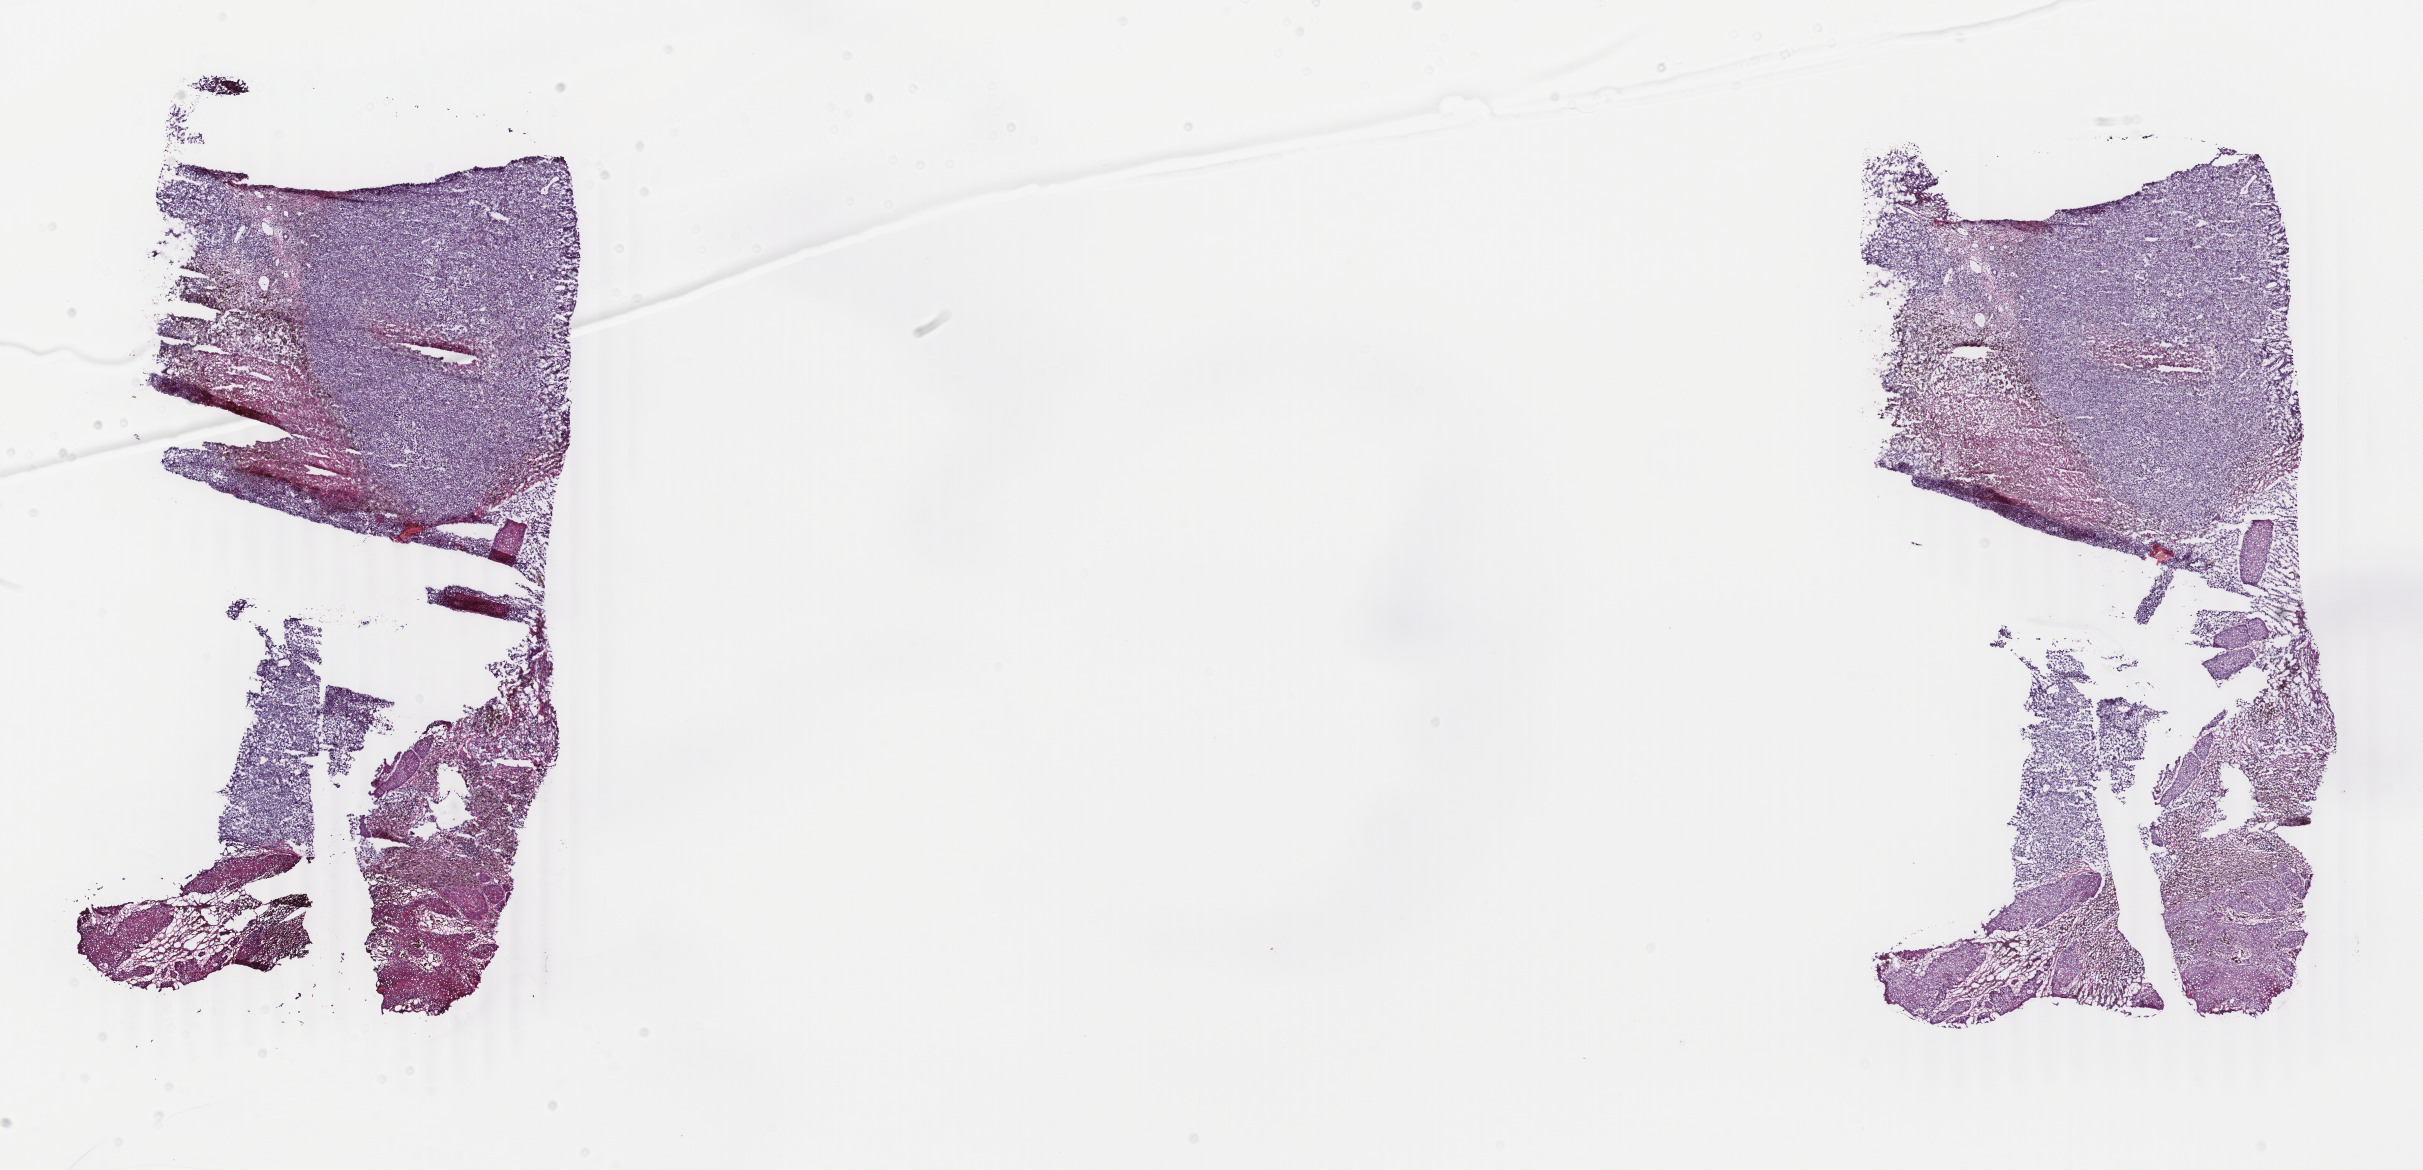
Hematoxylin and eosin (H&E) stained whole-slide image — whole scanned area (about 19.3 x 9.3 mm) shown as a low-resolution overview, frozen section from the top of the tissue portion, primary tumour sample from the skin. Male patient; age at initial diagnosis 56 years.
Diagnosis: Malignant melanoma, NOS.